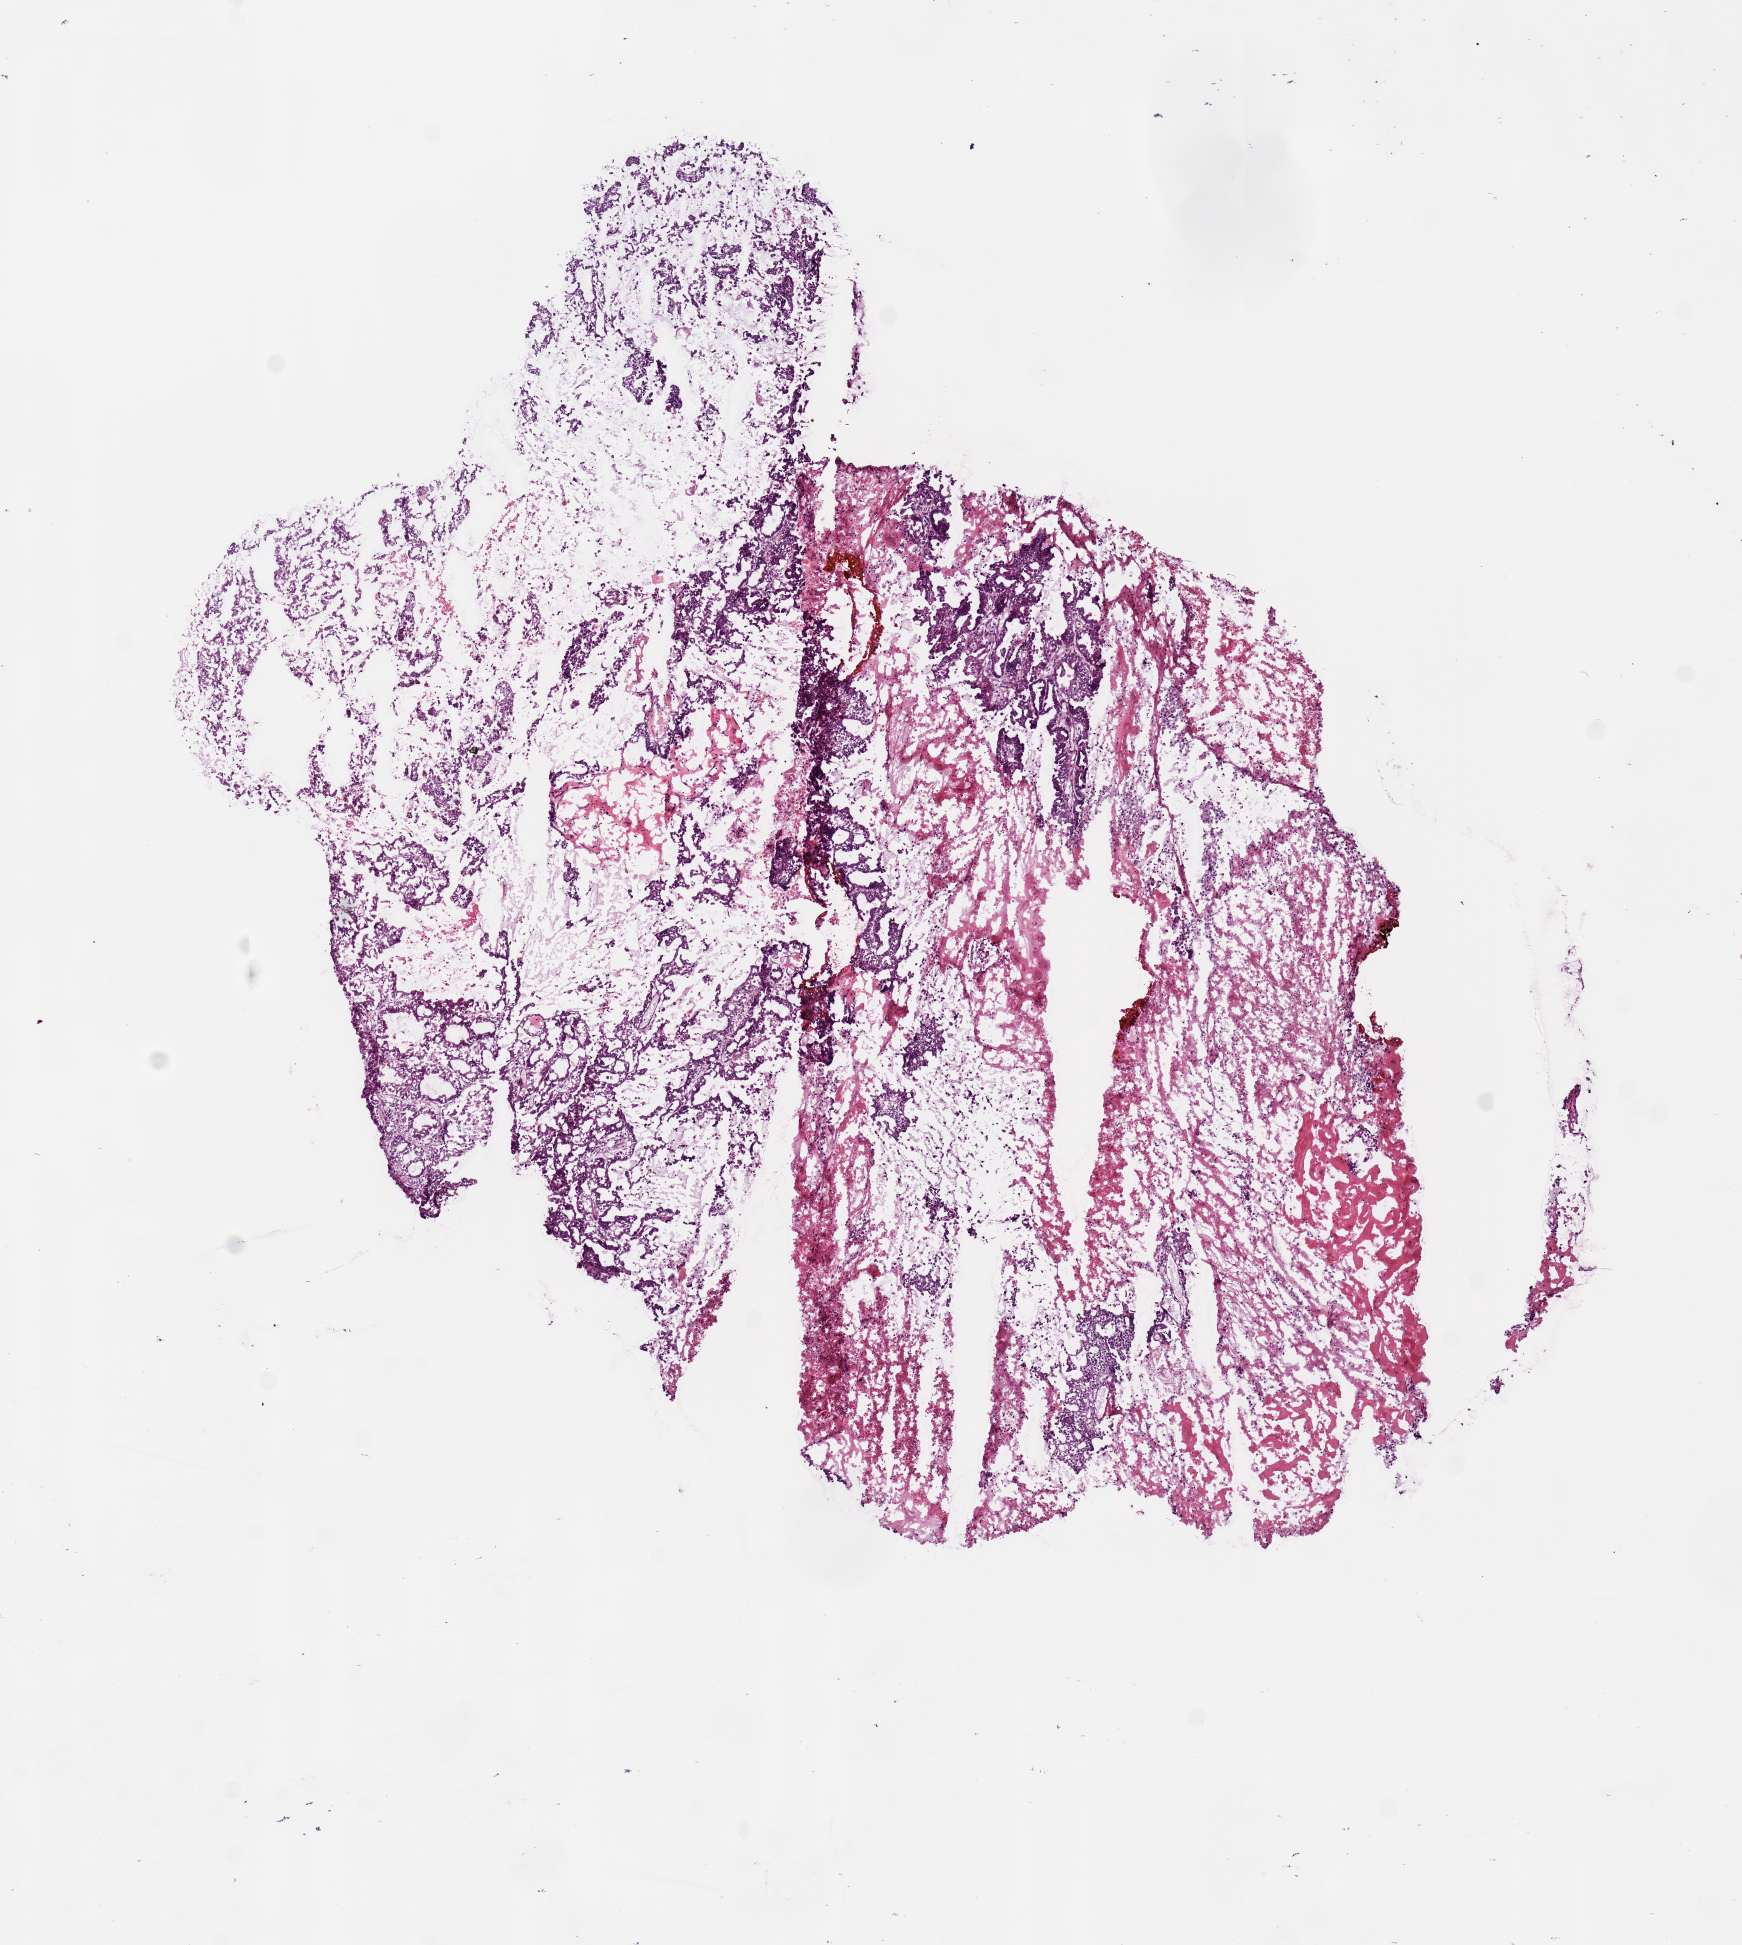
H&E-stained whole-slide image, whole scanned area (about 6.9 x 7.7 mm) shown as a low-resolution overview. Frozen section from the top of the tissue portion. Sample: primary tumour, uterus. Female patient; age at initial diagnosis 85 years. Histologic grade: G3 (poorly differentiated). Slide review estimates, as recorded: tumour cells 55%, tumour nuclei 65%, normal cells 0%, stromal cells 30%, necrosis 15%. Inflammatory infiltration, as recorded: lymphocyte infiltration 0%, monocyte infiltration 0%, neutrophil infiltration 0%.
Diagnosis: Endometrioid adenocarcinoma, NOS (endometrium). FIGO stage: IB.